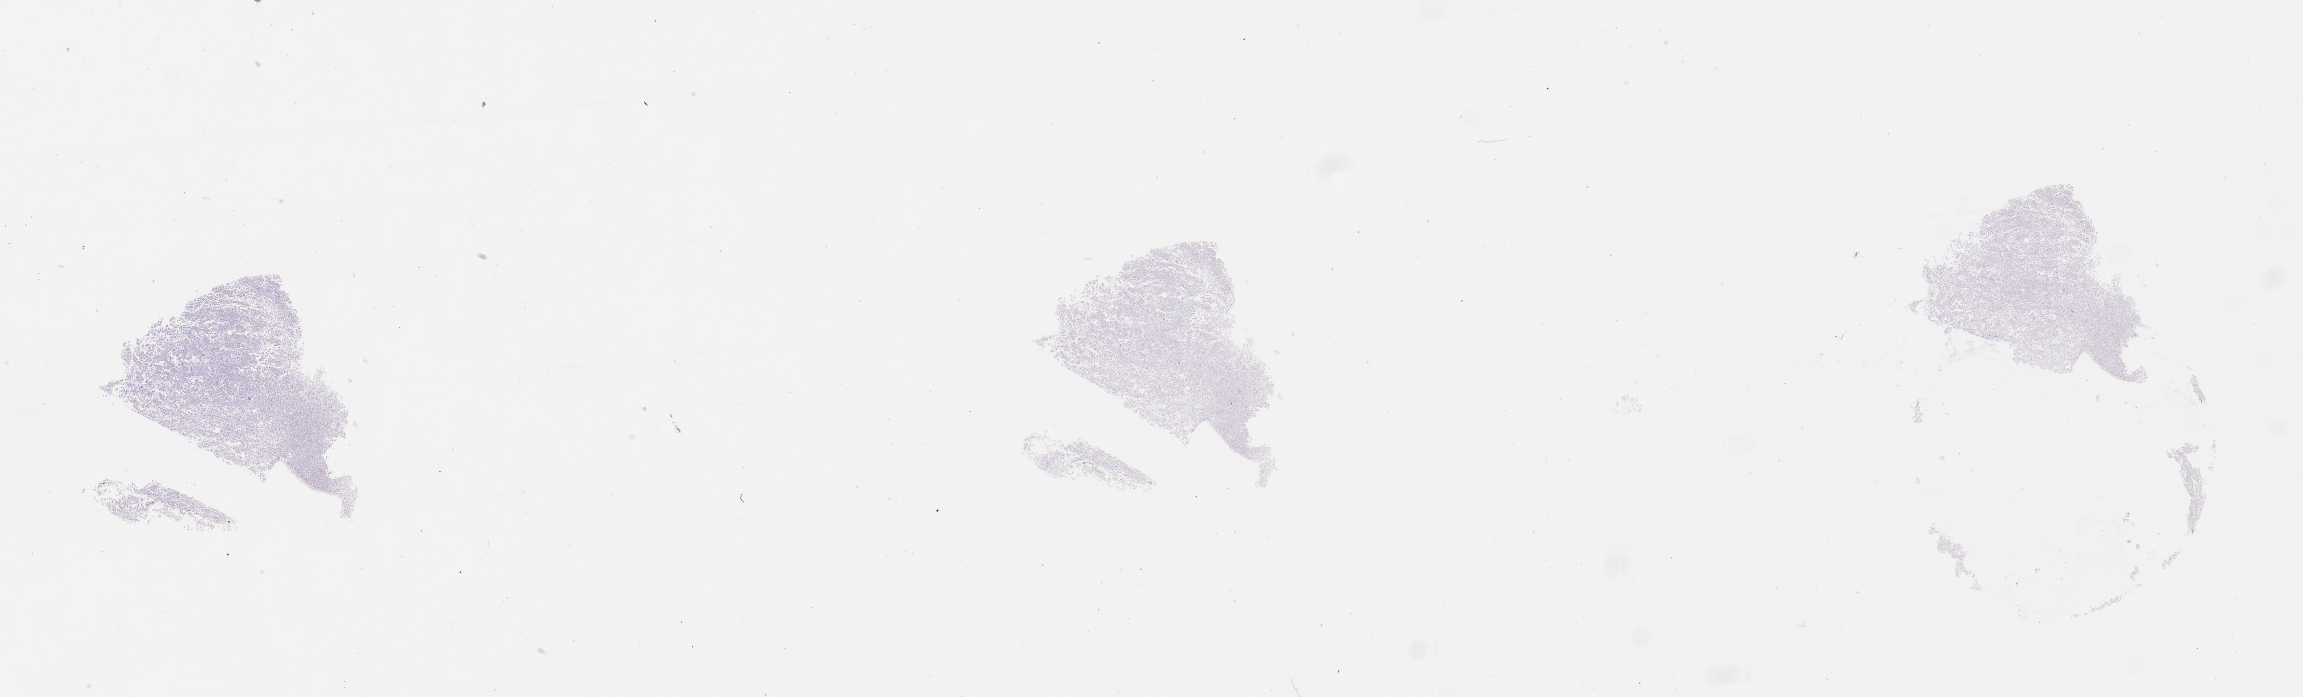
Digitized H&E tissue section (whole slide) — whole scanned area (about 37.1 x 11.2 mm) shown as a low-resolution overview. Tumour tissue sample, sampled site: brain. Male, 65 y/o.
Histologic diagnosis: Glioblastoma.